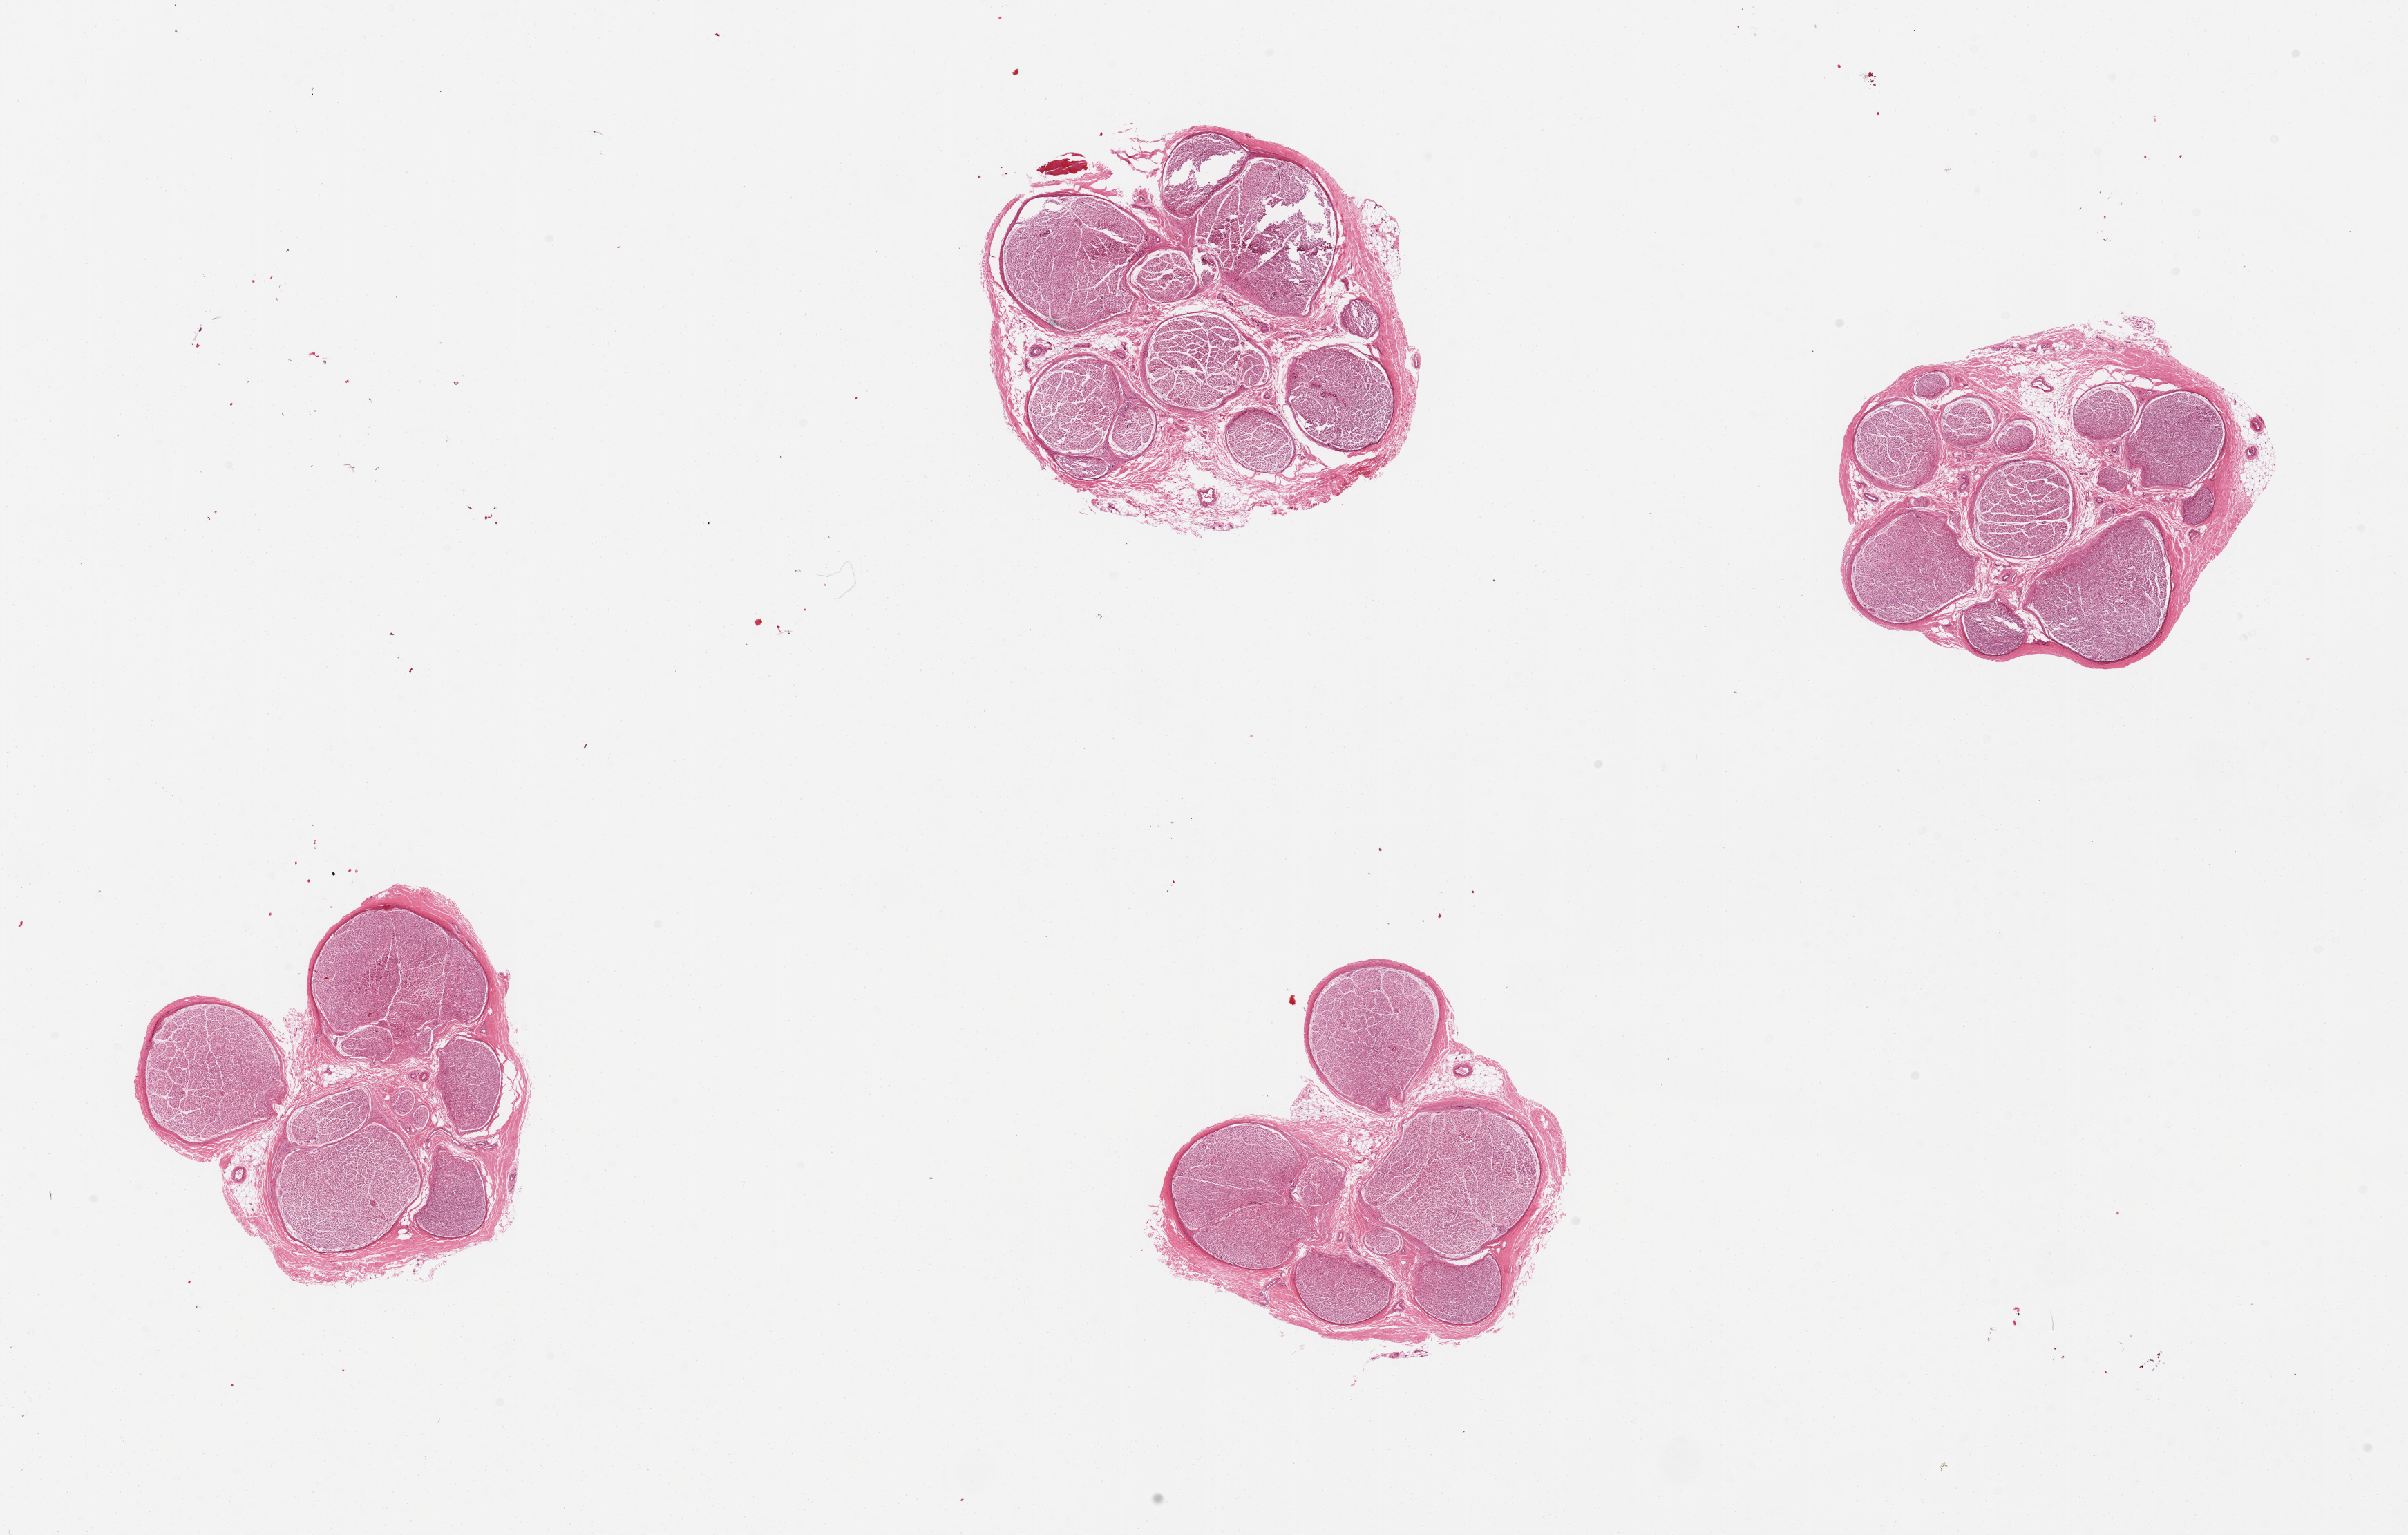
Whole-slide image, haematoxylin and eosin stain — low-resolution overview of the scanned area, about 27.6 x 17.6 mm (slide scanned at 20x); PAXgene-fixed paraffin-embedded (PFPE) section; sampled site (target tissue): tibial nerve; donor tissue sample. Donor: male.
Reviewer comment on this tissue sample: 4 pieces, clean specimens, no adherent fat.